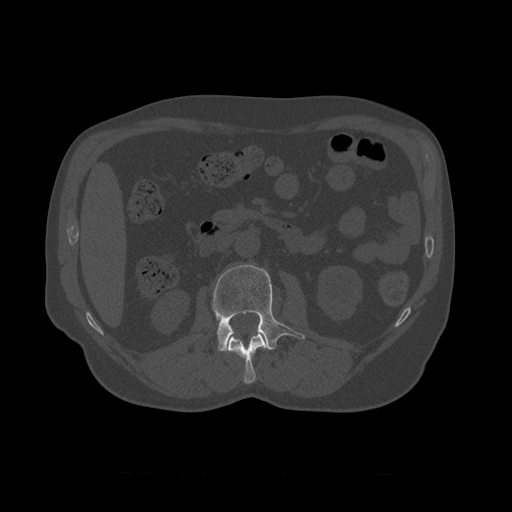
CT including the spine, one axial slice; slice 338 of 450 in the series (ordered by position); reconstruction kernel STANDARD; bone window (W 1800 / L 400 HU); 1.25 mm slice thickness; 512 × 512 image matrix. Patient age 75 years. Case-level facts recorded for this patient, not image findings: primary cancer: prostate.
Outlined on this slice (semi-automatically segmented with operator editing):
- L1 vertebra: box from (x=227, y=331) to (x=269, y=384) px
- L2 vertebra: (x=212, y=265)–(x=305, y=352)